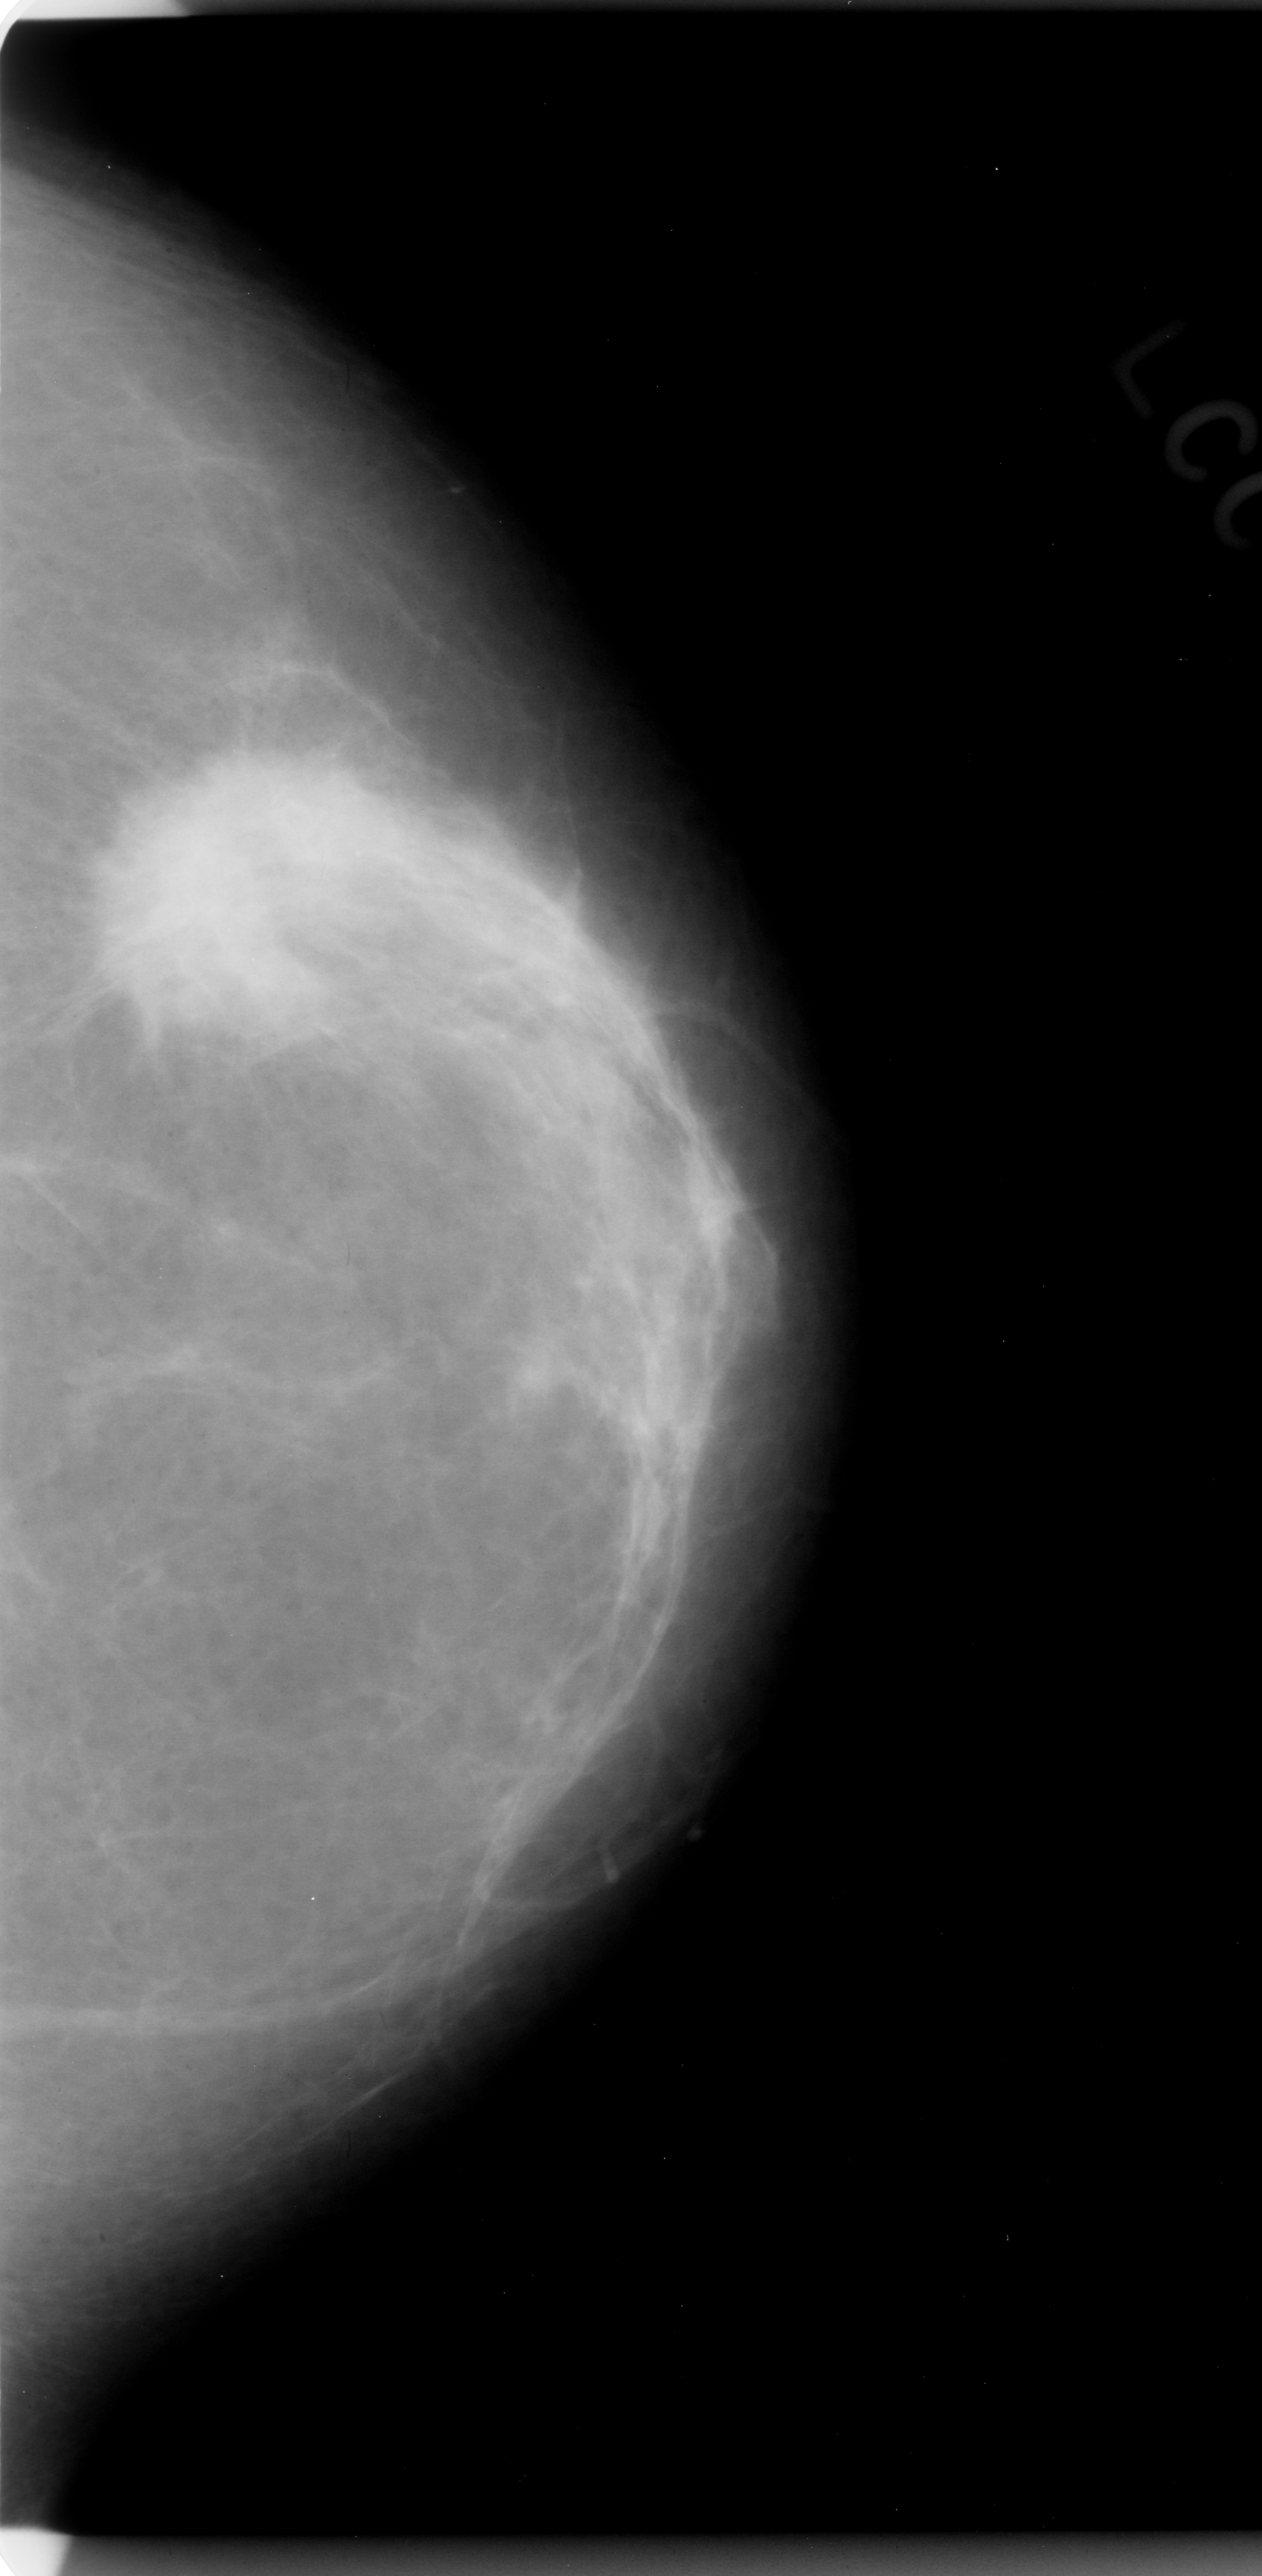
Mammogram (digitized film), left breast, CC view, BI-RADS breast density category 2 (scale 1–4).
- Mass, shape irregular, margins spiculated; BI-RADS assessment category 5; subtlety rating 5 on a 1 (subtle) to 5 (obvious) scale; pathology (as recorded): malignant.